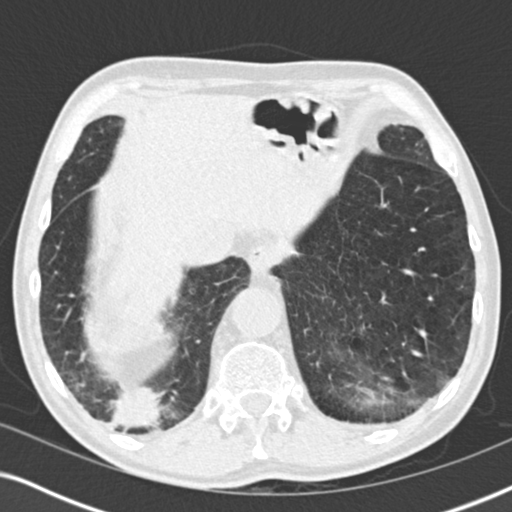
Low-dose screening chest CT, axial slice; first (baseline) screen; lung window (W 1500 / L -600 HU); standard (soft-tissue) reconstruction kernel (B30f); slice 146 of 196 in the series. Male participant, aged 64 years at enrolment.
- Expert reader's lesion annotation, box from (x=75, y=363) to (x=180, y=453) px.
- The screening reader recorded 3 non-calcified nodules or masses ≥4 mm on this exam (lingula, lingula, right lower lobe); which of them this box marks is not recorded.
- Official screen result: positive, change unspecified: nodule(s) >= 4 mm or enlarging nodule(s), mass(es), or other non-specific abnormalities suspicious for lung cancer.
- Participant outcome: lung cancer diagnosed 27 days after this screen — squamous cell carcinoma, NOS, right lower lobe, moderately differentiated (G2), stage IV (AJCC 6th edition), 40 mm at pathology.